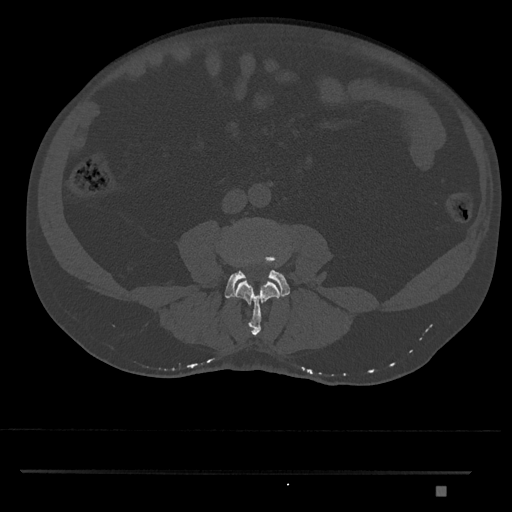
CT including the spine, one axial slice; slice 650 of 1134 in the series (ordered by position); reconstruction kernel Br40s/3; bone window (W 1800 / L 400 HU); 512 × 512 image matrix, field of view 429 × 429 mm. Patient: male, 65 years. Case-level facts recorded for this patient, not image findings: primary cancer: prostate.
Structures marked on this image (semi-automatic segmentation, software-assisted and operator-edited):
- L3 vertebra: bounding box <235,281,280,337> (left, top, right, bottom; pixels)
- L4 vertebra: <225,250,290,299>